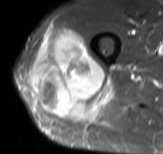
MRI of an extremity soft-tissue mass, one axial slice. Slice 42 of 61 in the series (ordered by position). STIR. MR volume resampled by the dataset authors to the PET/CT grid (not the native acquisition matrix). 163 × 154 image matrix, field of view 159 × 150 mm. Male patient. From the clinical record (not read from this slice): histological type: poorly differentiated synovial sarcoma; grade: high; site of the primary tumour: right buttock.
Outlined on this slice (expert contour drawn on MRI and transferred to this co-registered scan by the dataset authors):
- gross tumour volume including surrounding oedema: box from (x=29, y=27) to (x=108, y=120) px
- gross tumour volume (mass): (x=29, y=27)–(x=106, y=120)